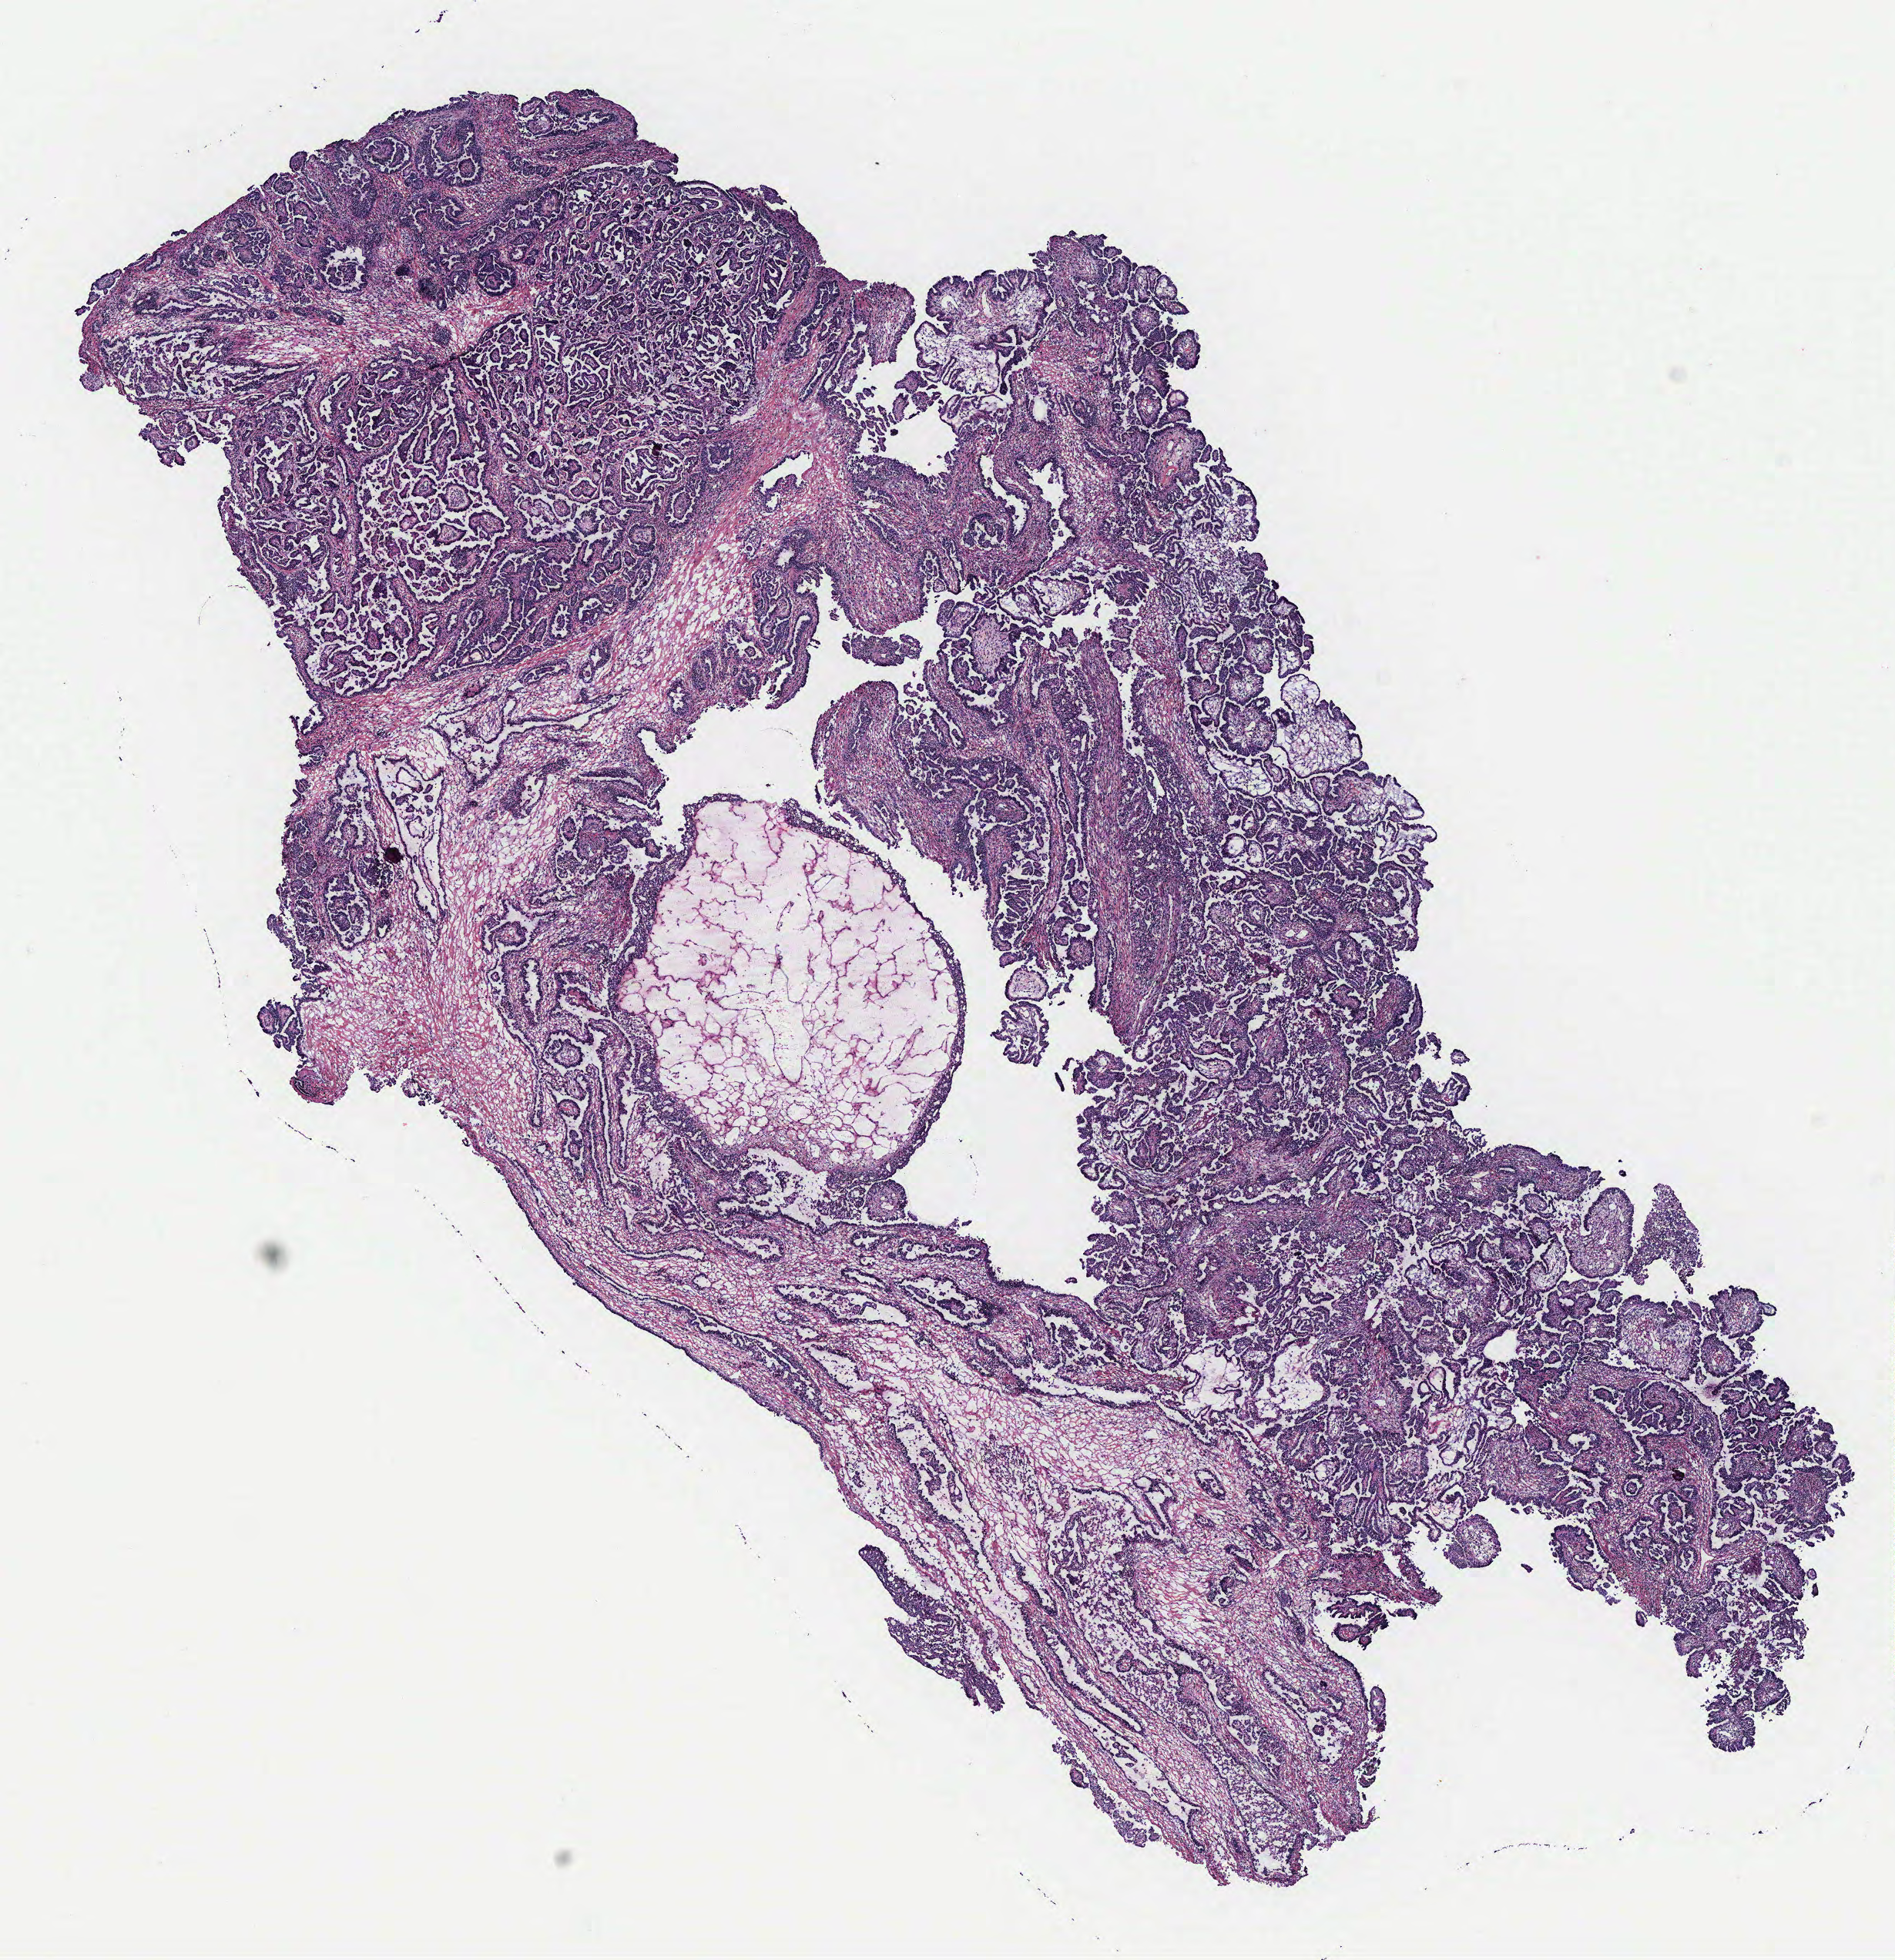
H&E whole-slide image, low-resolution overview of the scanned area, about 9.8 x 10.2 mm (slide scanned at 40x). Tumour tissue sample, ovary. Female, 46 y/o.
* histologic diagnosis: Serous adenocarcinoma, NOS
* primary tumour site (as recorded): ovary